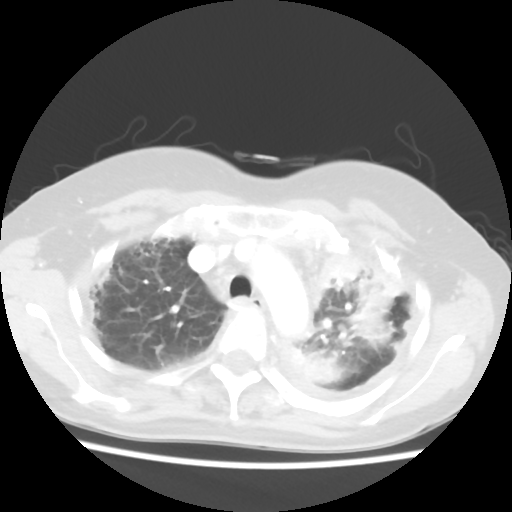
Chest CT, one axial slice; position 43 of 56 along the scan axis; 120 kVp; lung window (W 1500 / L -600 HU); 5 mm slice thickness; 512 × 512 image matrix, field of view 309 × 309 mm. Female patient, age 56 years. Case-level facts recorded for this patient, not image findings: clinical TNM (as recorded): T1c N0 M1.
Outlined on this slice (rectangle marked by the reading radiologist):
- lung tumour (recorded histology: adenocarcinoma): box from (x=316, y=247) to (x=367, y=297) px